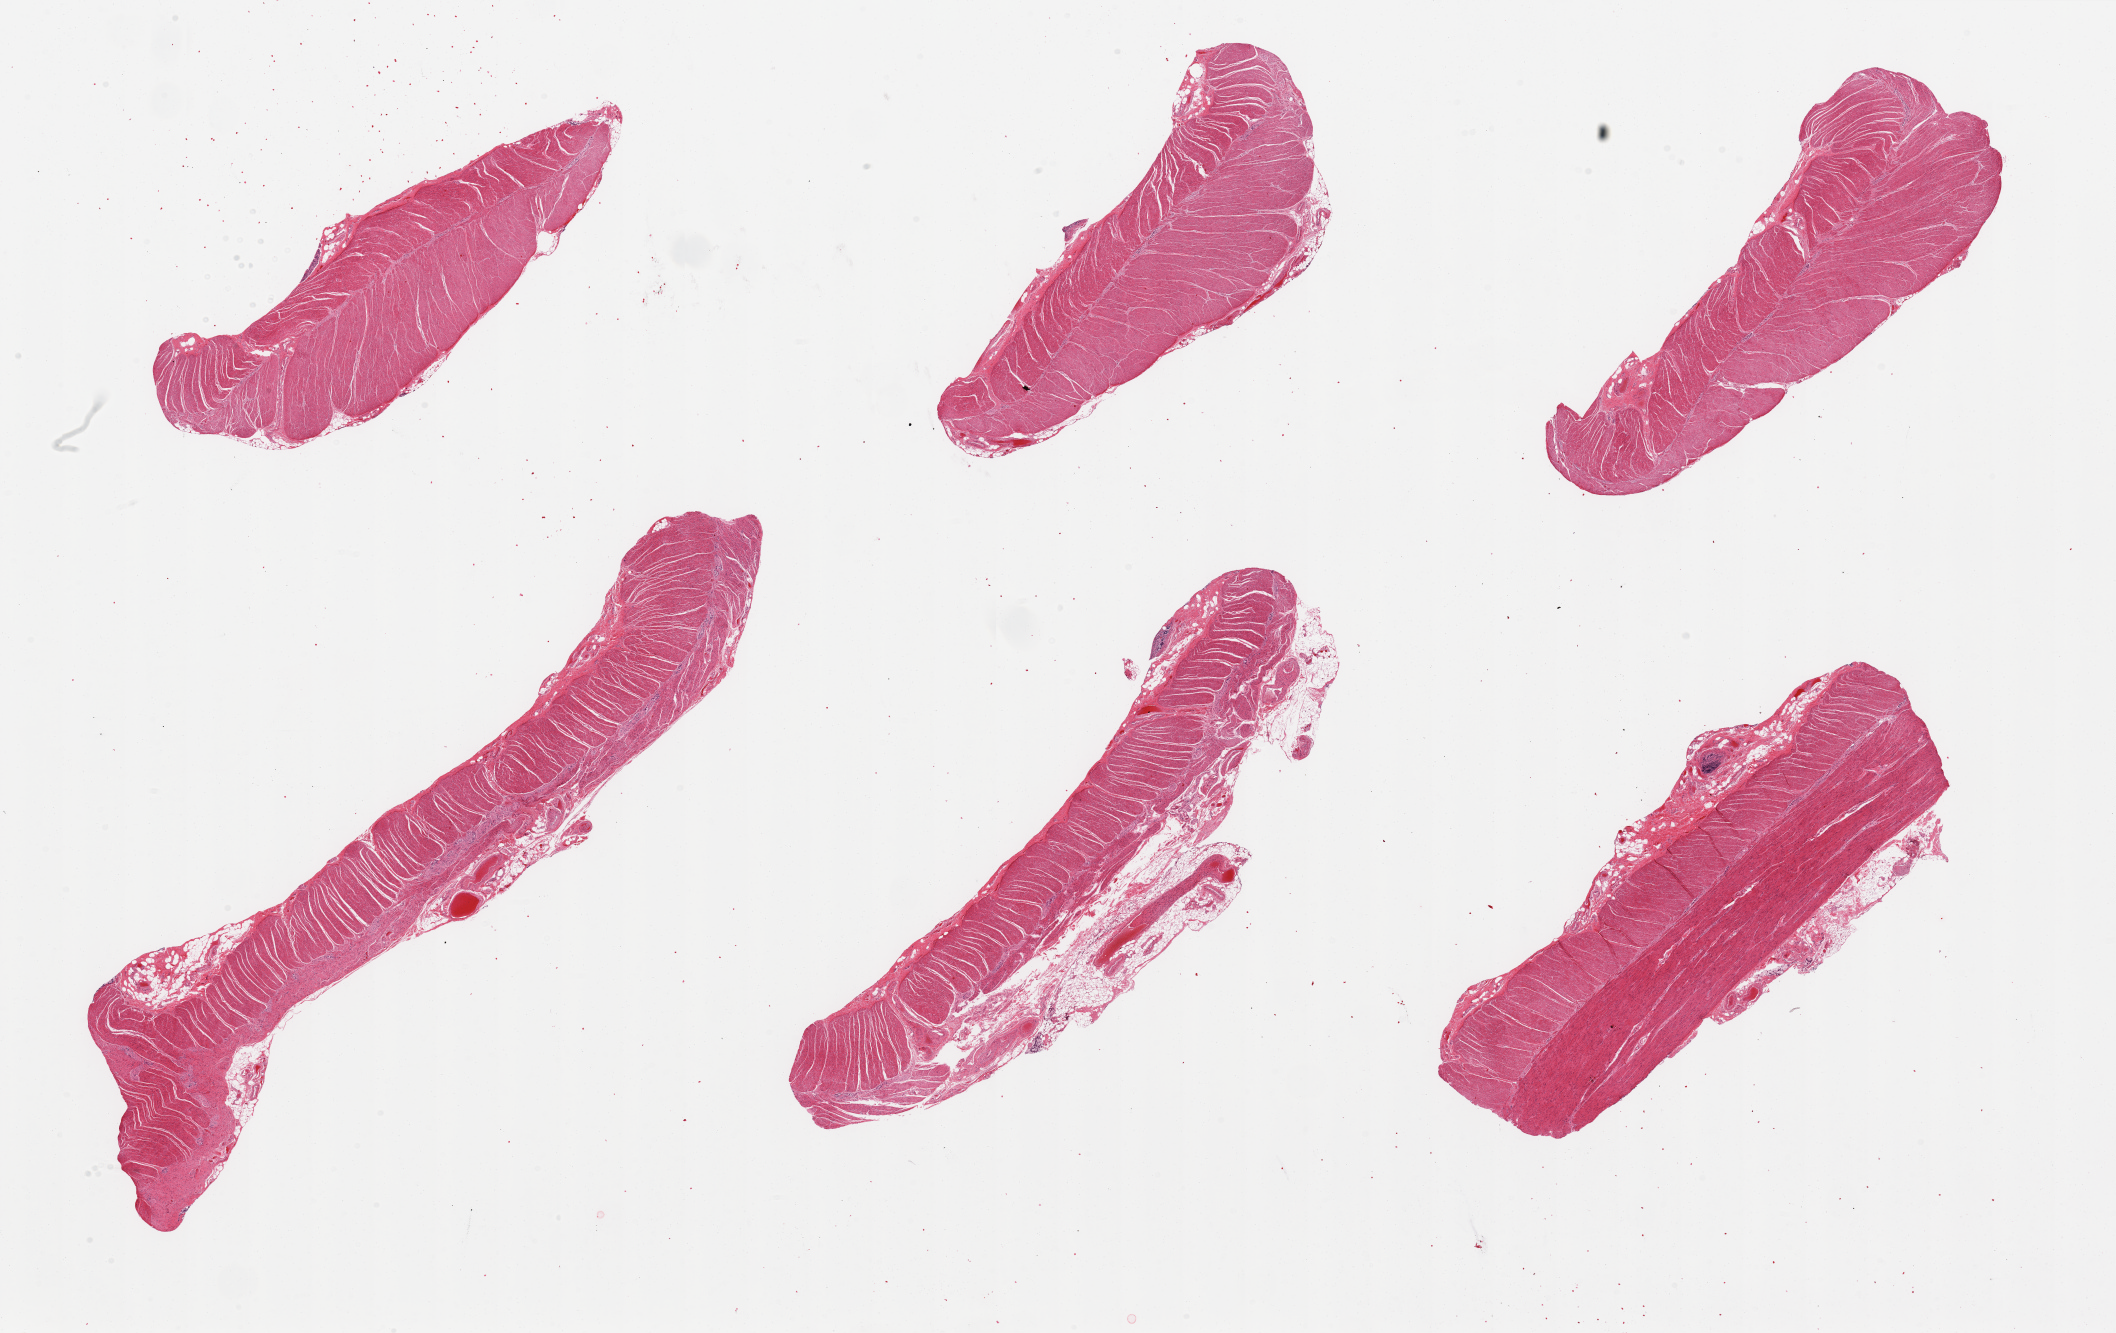
Digitized hematoxylin and eosin (H&E)-stained section, shown as a low-resolution overview of the whole scanned area (about 33.5 x 21.1 mm). PAXgene-fixed paraffin-embedded (PFPE) section. Target tissue: sigmoid colon. Tissue donor sample. Donor: female.
Reviewer comment on this tissue sample: 6 pieces, all muscularis, good specimens.